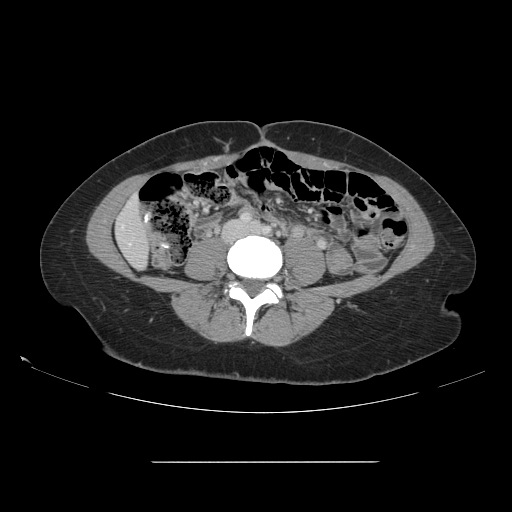
Contrast-enhanced abdominal CT, one axial slice. Slice 18 of 151 in the series (ordered by position). 120 kVp. Intravenous contrast given. Soft-tissue window (W 400 / L 40 HU). 2.5 mm slice thickness. 512 × 512 image matrix. Female patient, age 46 years. Case-level facts recorded for this patient, not image findings: diagnosis: colorectal cancer liver metastases, imaged before liver resection; multiple liver metastases: yes; largest metastasis: 3 cm; disease in both lobes: yes.
Outlined on this slice (manually delineated by an expert):
- liver: box from (x=117, y=199) to (x=149, y=268) px
- planned liver remnant (the part of the liver to remain after resection): (x=117, y=199)–(x=149, y=268)